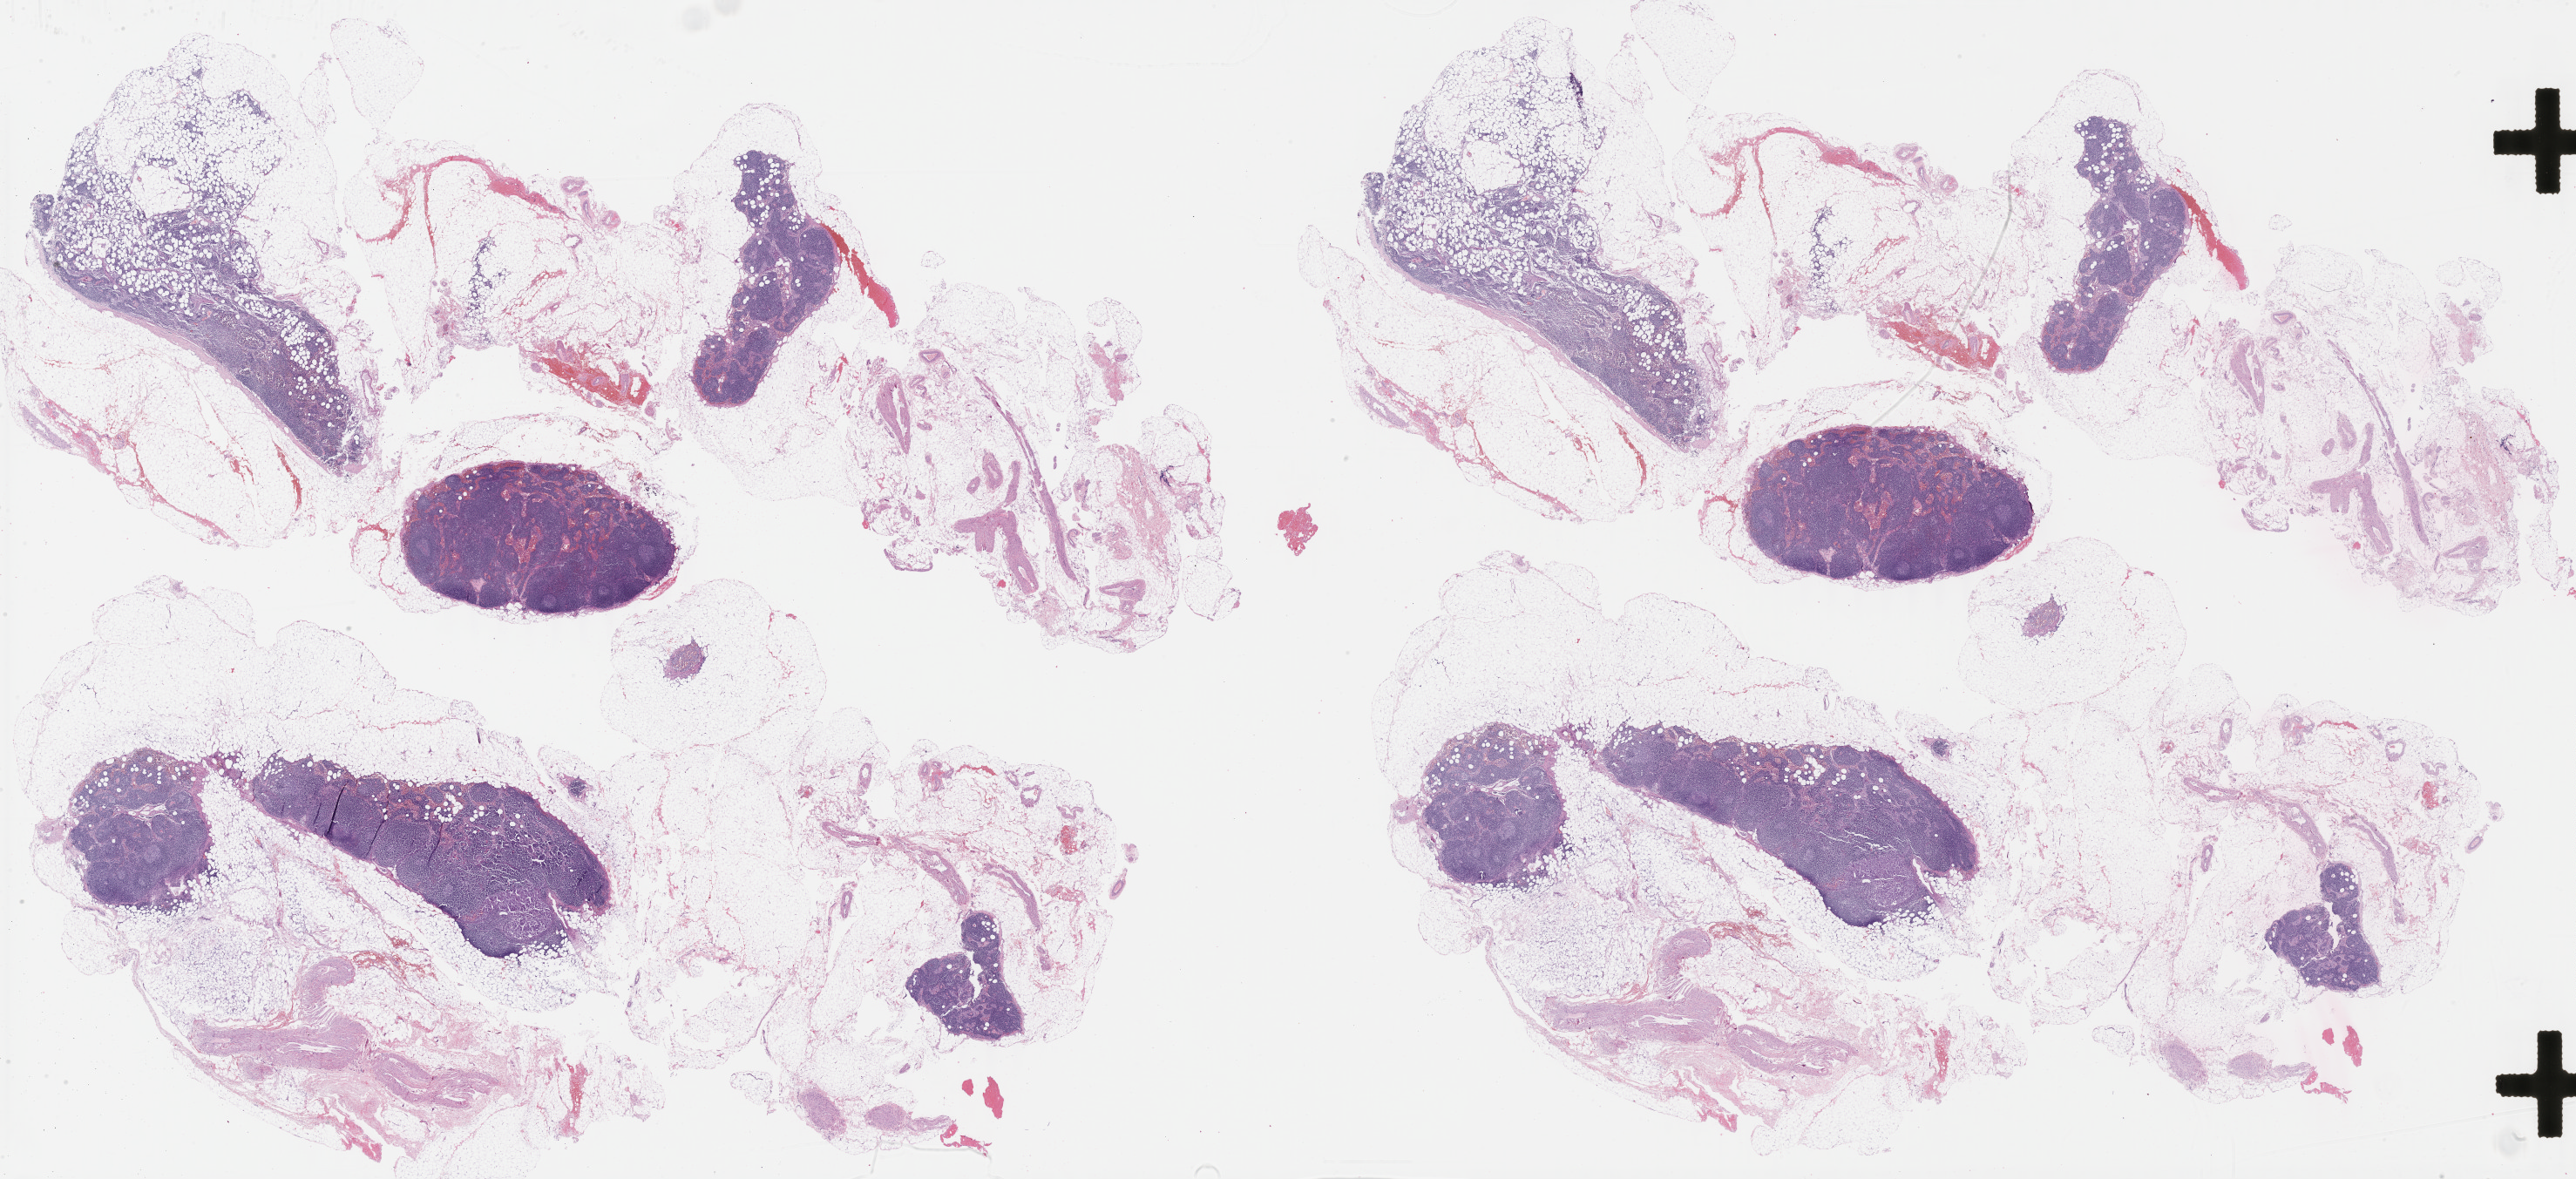
Hematoxylin and eosin (H&E) stained whole-slide image — shown as a low-resolution overview of the whole scanned area (about 47.8 x 21.9 mm, slide scanned at 40x); FFPE section; primary tumour sample from the uterus. Female, age 61 years at initial diagnosis. Histologic grade: G3 (poorly differentiated).
• FIGO stage: IIIC1
• pathologic diagnosis: Serous cystadenocarcinoma, NOS (endometrium)